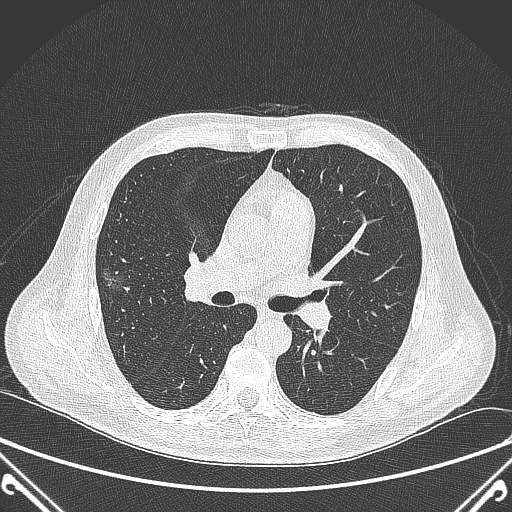
Chest CT, one axial slice; slice 218 of 360 in the series (ordered by position); 120 kVp; lung window (W 1500 / L -600 HU); 512 × 512 image matrix. Patient: male, 64 years. From the clinical record (not read from this slice): clinical TNM (as recorded): T1c N0 M0; histopathological grade: G2.
Annotated regions visible in this slice (bounding box drawn by a radiologist):
- lung tumour (recorded histology: adenocarcinoma): bounding box (x1, y1, x2, y2) in pixels: (99, 262, 132, 300)